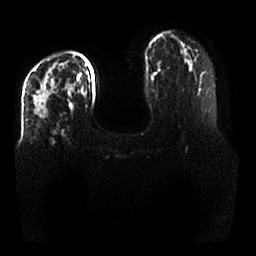
Breast MRI, one axial slice; position 16 of 25 along the scan axis; diffusion-weighted series; image 2 of 4 stored at this slice position (different b-values; order by instance number); 1.5 T; 4 mm slice thickness; 256 × 256 image matrix. Female patient.
Outlined on this slice (manually delineated by an expert):
- tumour on diffusion-weighted imaging: bounding box (x1, y1, x2, y2) in pixels: (33, 78, 54, 123)